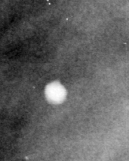
Region of interest cut from a scanned film mammogram (one marked finding); right breast; MLO view; BI-RADS breast density category 3 (scale 1–4).
Finding: calcifications, morphology round and regular / lucent center; BI-RADS assessment category 2; subtlety rating 4 on a 1 (subtle) to 5 (obvious) scale; benign without callback (not worked up further).